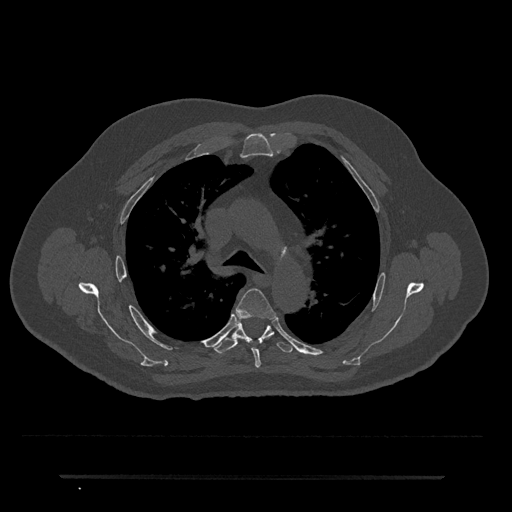
CT including the spine, one axial slice; slice 506 of 797 in the series (ordered by position); 120 kVp; bone window (W 1800 / L 400 HU); 512 × 512 image matrix, field of view 437 × 437 mm. Male patient, age 69 years. Case-level facts recorded for this patient, not image findings: primary cancer: prostate.
Annotated regions visible in this slice (semi-automatic segmentation, software-assisted and operator-edited):
- T4 vertebra: bounding box <236,288,276,368> (left, top, right, bottom; pixels)
- T5 vertebra: <212,321,293,354>